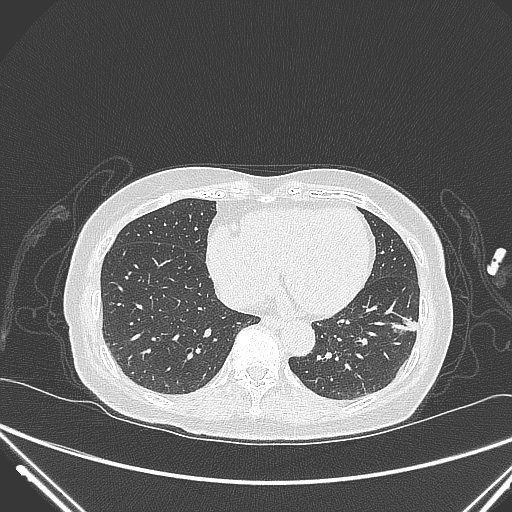
Chest CT, one axial slice. Position 103 of 310 along the scan axis. 120 kVp. Lung window (W 1500 / L -600 HU). 1 mm slice thickness. 512 × 512 image matrix. Female patient, age 82 years. Case-level facts recorded for this patient, not image findings: clinical TNM (as recorded): T1c N0 M0.
Structures marked on this image (rectangle marked by the reading radiologist):
- lung tumour (recorded histology: adenocarcinoma): bounding box [x1, y1, x2, y2] px = [389, 313, 430, 349]